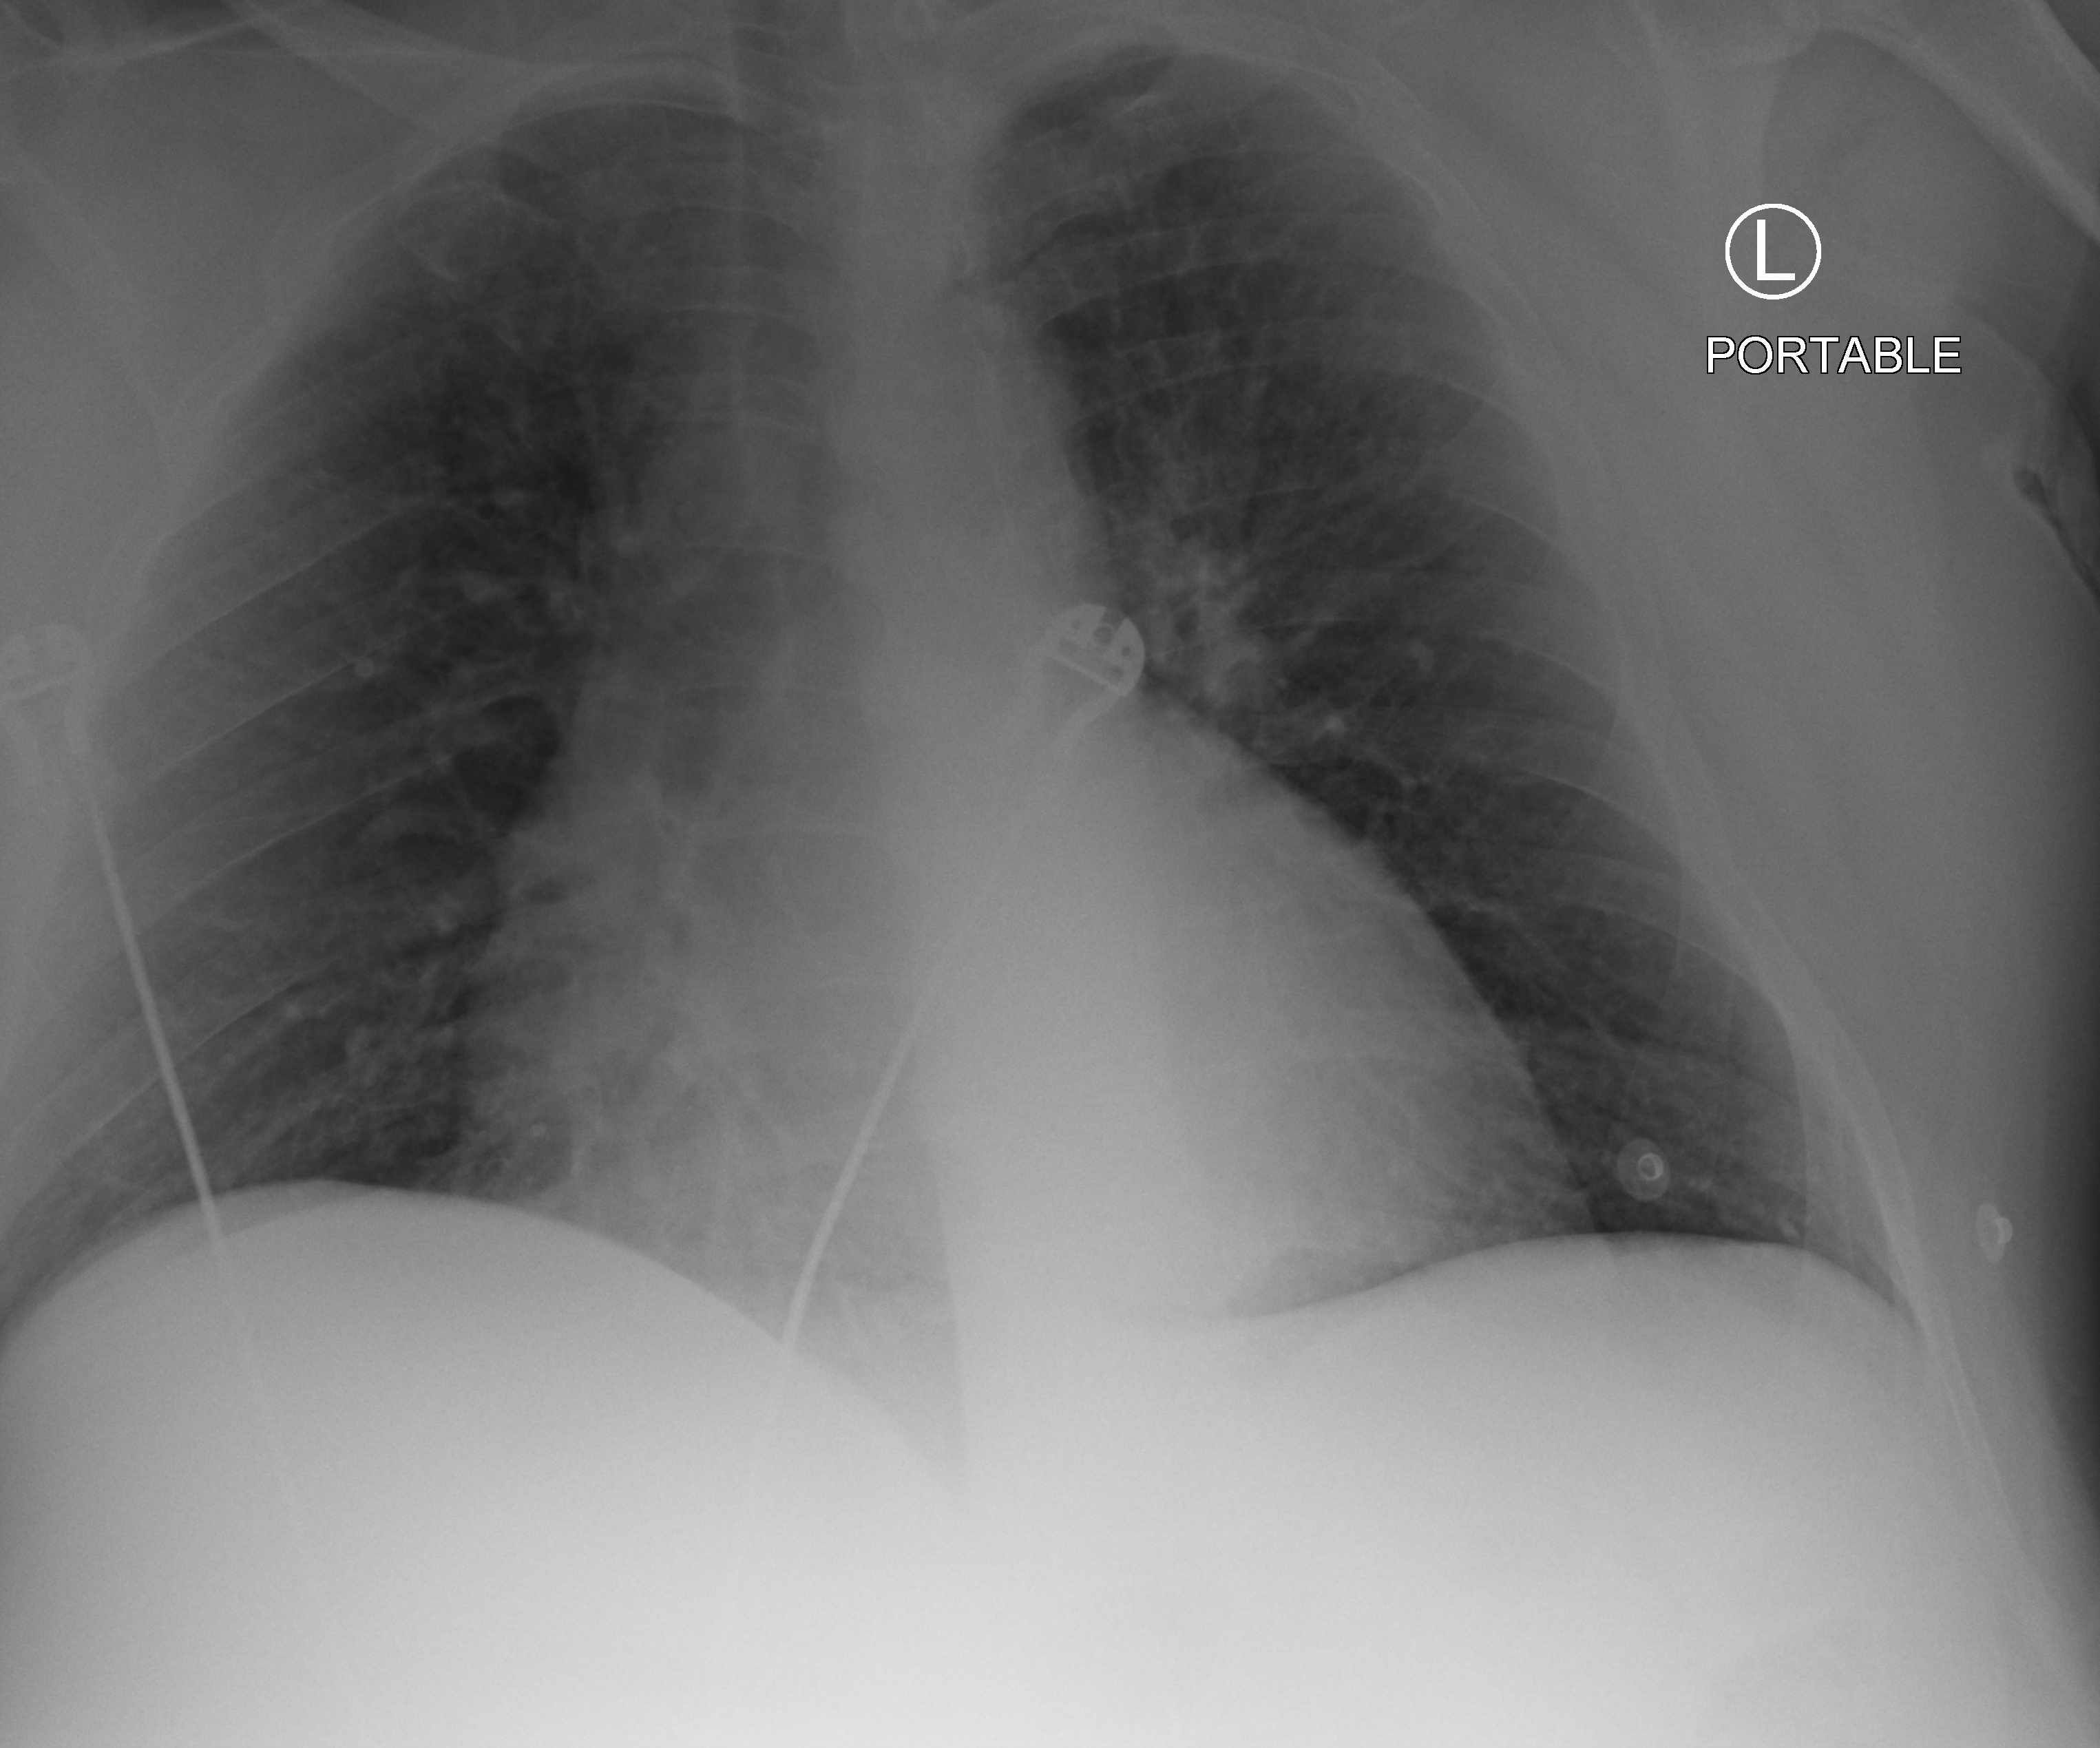
Portable chest radiograph; anteroposterior (AP) projection. Male patient hospitalised with COVID-19, age 18–59 years.
Hospital-stay facts (about this admission, not read from this image; timing relative to this image not recorded): length of hospital stay: 2 days.